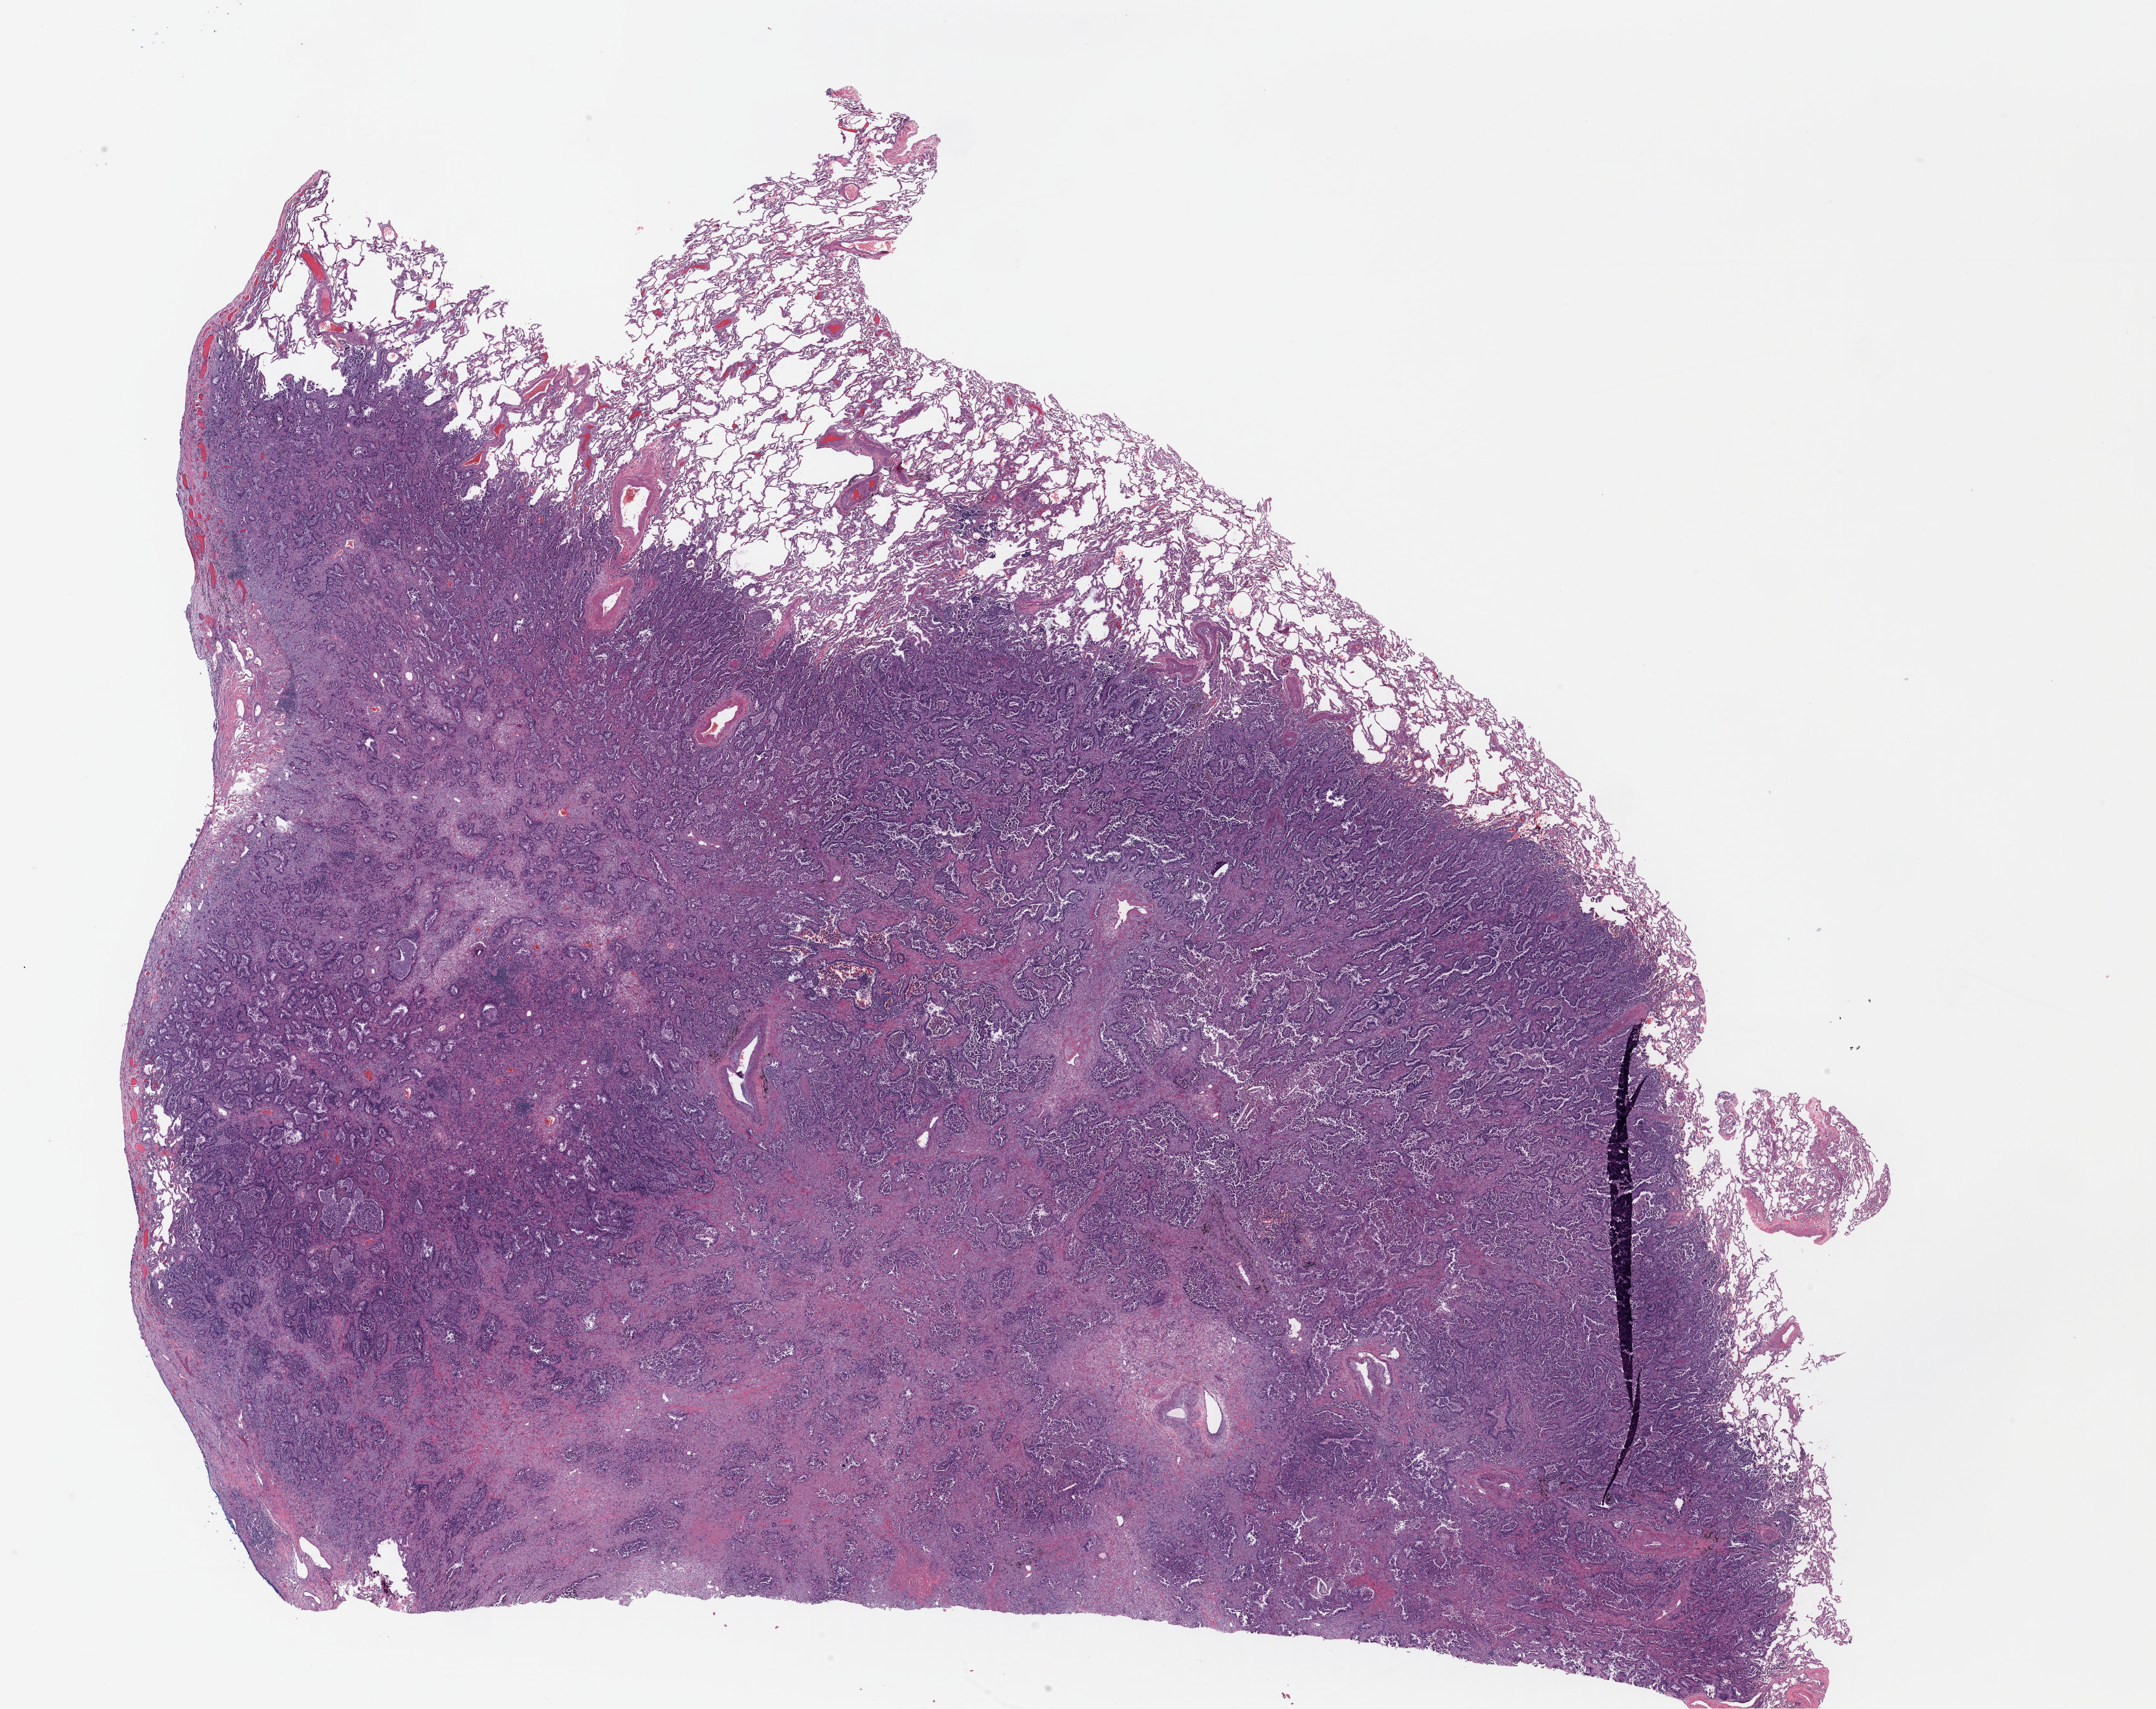
Digitized H&E tissue section (whole slide) — shown as a low-resolution overview of the whole scanned area (about 26.2 x 20.8 mm). Formalin-fixed paraffin-embedded (FFPE) diagnostic section. Primary tumour sample from the lung. Male, age 65 years at initial diagnosis.
Histologic diagnosis: Invasive micropapillary carcinoma. TNM: T2a N0 MX. Laterality: left. AJCC pathologic stage: IB (7th edition).